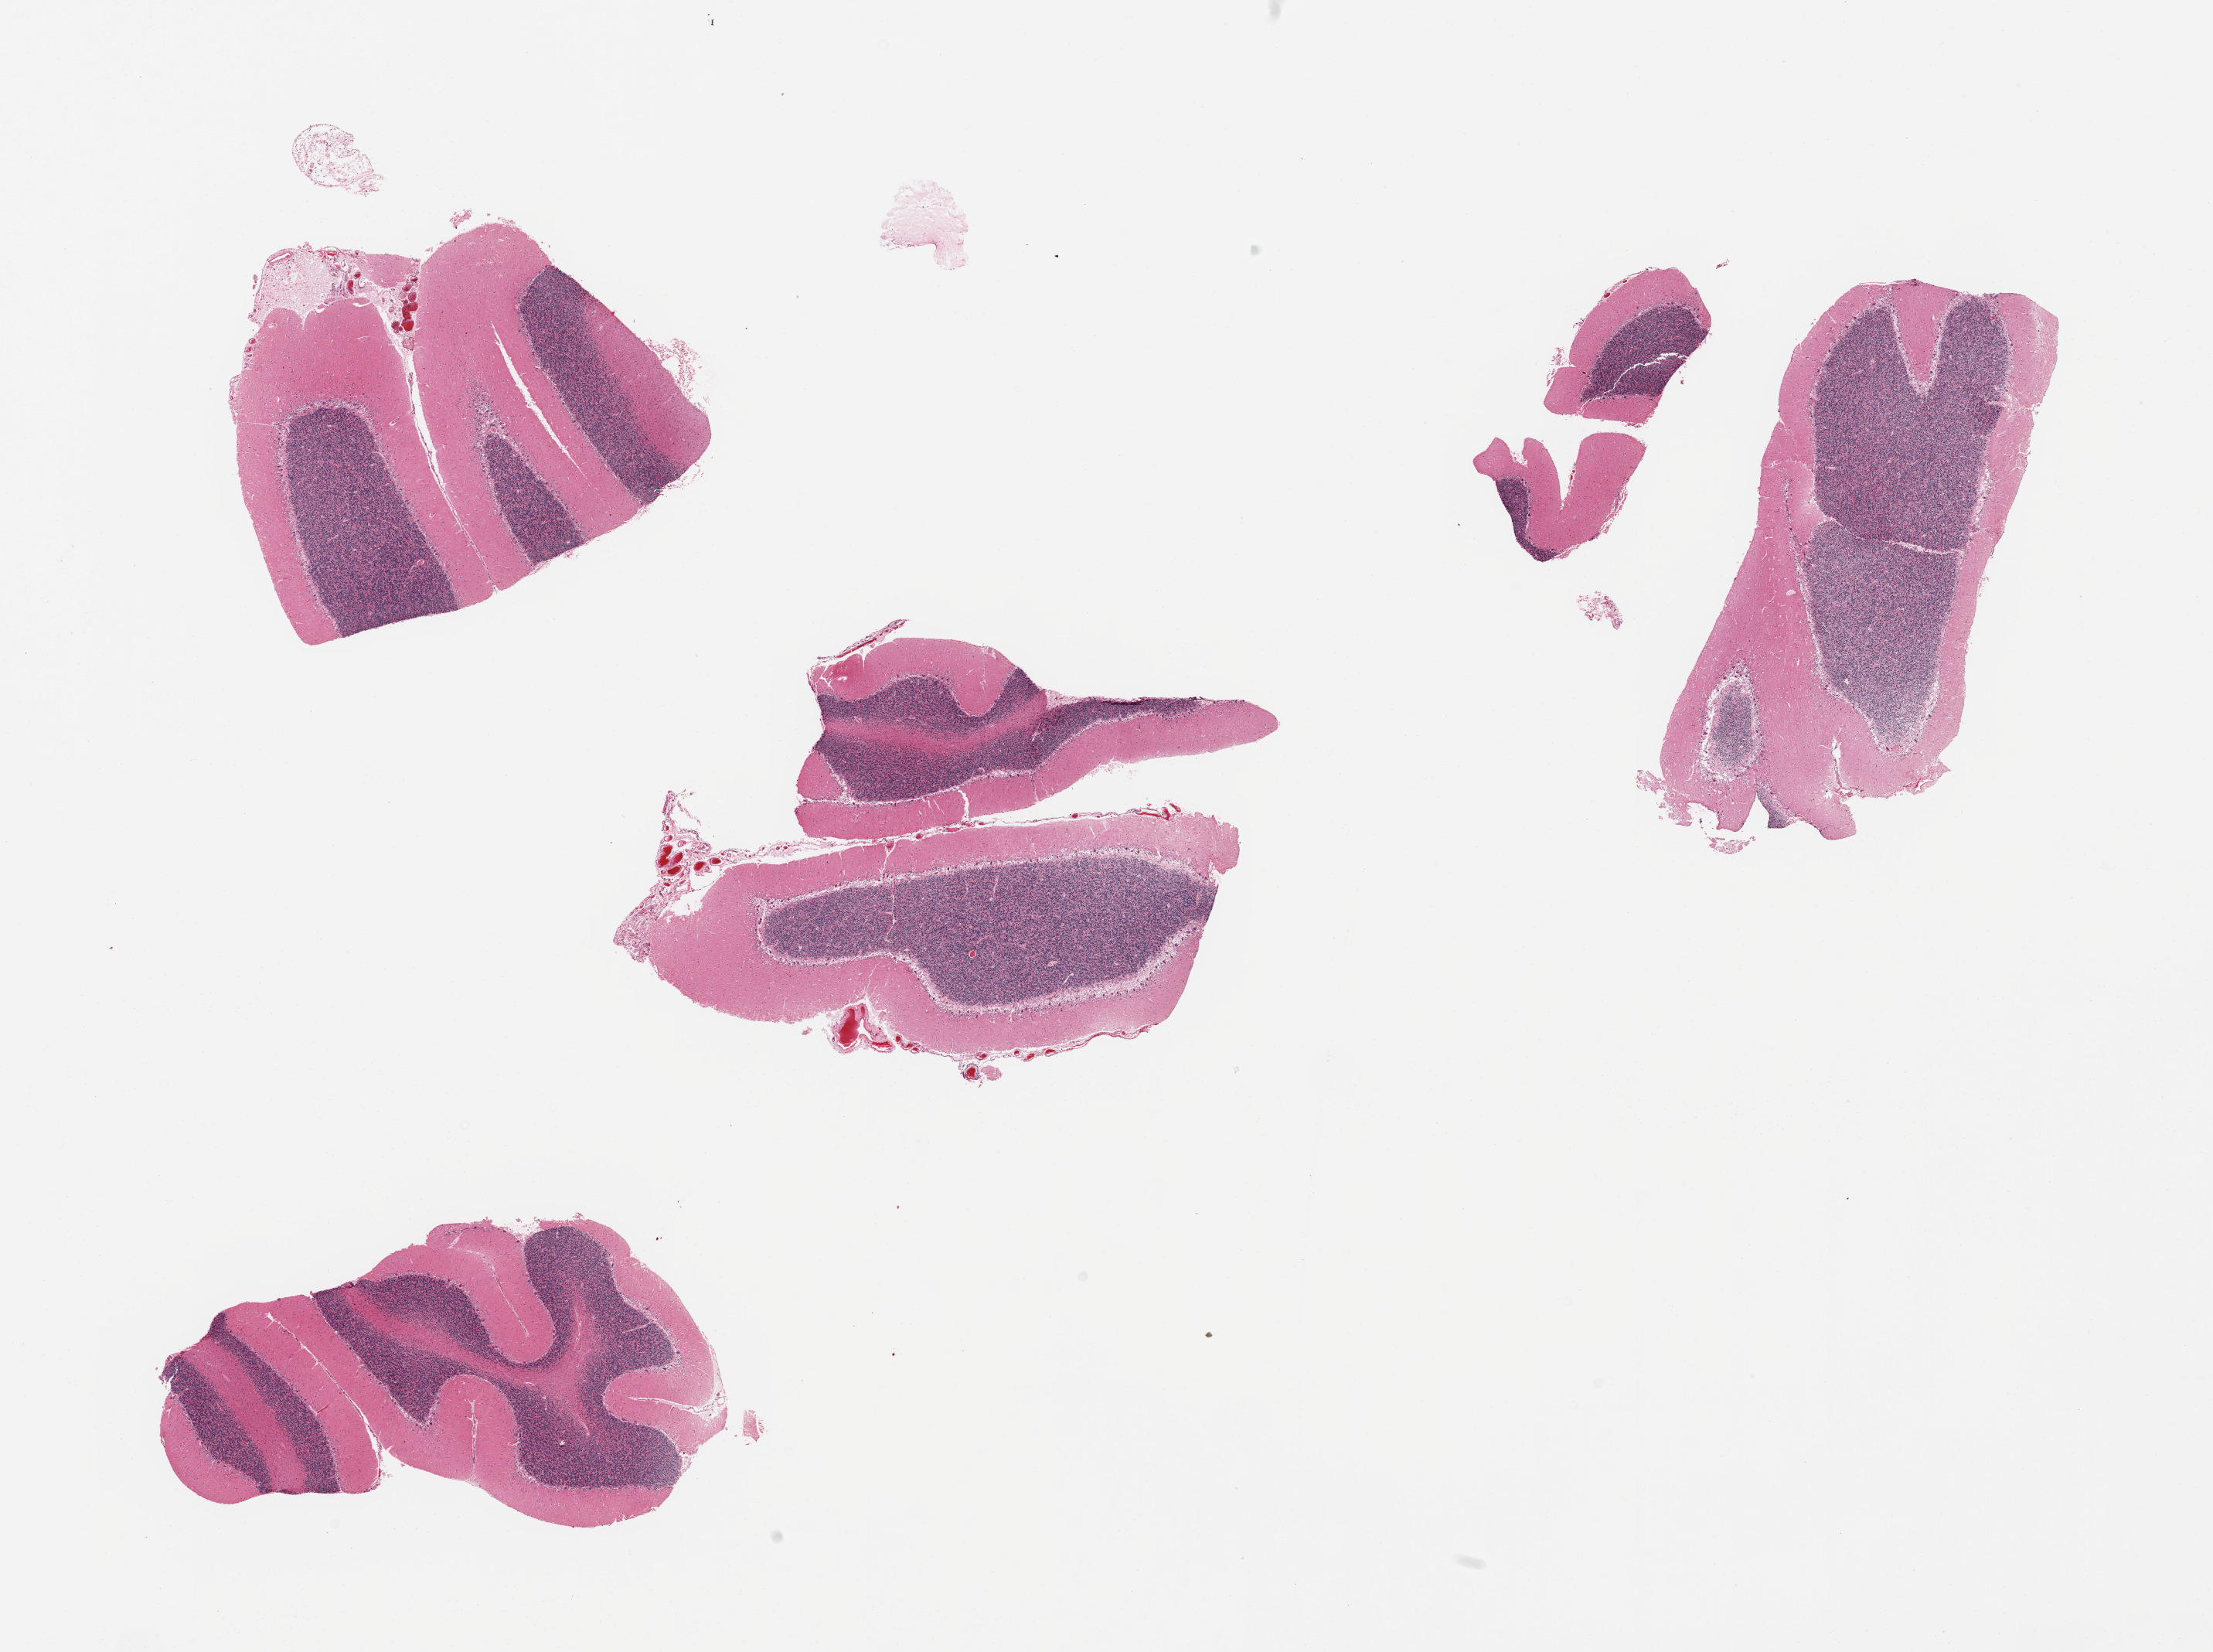
Whole-slide image, H&E stain, low-resolution overview of the scanned area, about 22.6 x 16.9 mm, PAXgene-fixed, paraffin-embedded tissue, target tissue: cerebellum, donor tissue sample. Donor: female.
Pathologist's review note for this sample: 6 pieces; Purkinje cells well visualized and with evidence of hypoxic damage, some attached meninges.